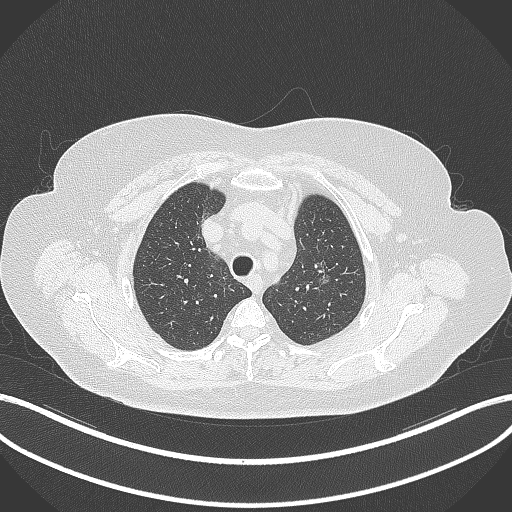
Chest CT, one axial slice; position 273 of 309 along the scan axis; reconstruction kernel B70f; 120 kVp; lung window (W 1500 / L -600 HU); 512 × 512 image matrix, field of view 400 × 400 mm. Patient: female, 70 years. From the clinical record (not read from this slice): clinical TNM (as recorded): T1c N0 M0.
Structures marked on this image (bounding box drawn by a radiologist):
- lung tumour (recorded histology: adenocarcinoma): bounding box <309,261,334,291> (left, top, right, bottom; pixels)